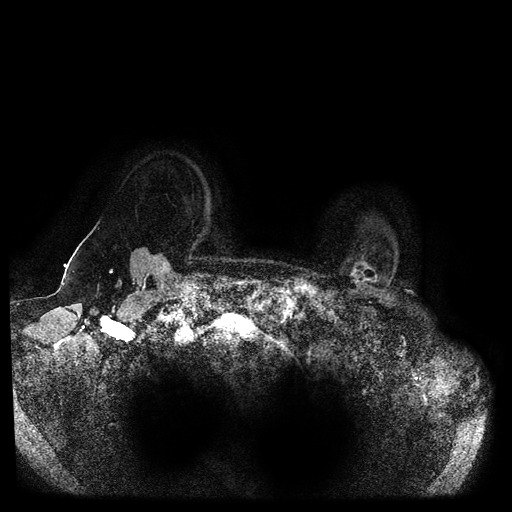
Breast MRI (dynamic contrast-enhanced, multi-phase), one axial slice. Slice 90 of 116 in the series (ordered by position). Dynamic contrast-enhanced series, time point 2 of 5 at this slice position (early post-contrast). 1.5 T. TE 2.6 ms, TR 5.3 ms. 2 mm slice thickness. 512 × 512 image matrix, field of view 370 × 370 mm. Female patient, age 55 years.
Structures marked on this image (semi-automatic segmentation, software-assisted and operator-edited):
- breast lesion (labelled benign in the annotation): box from (x=349, y=259) to (x=382, y=288) px